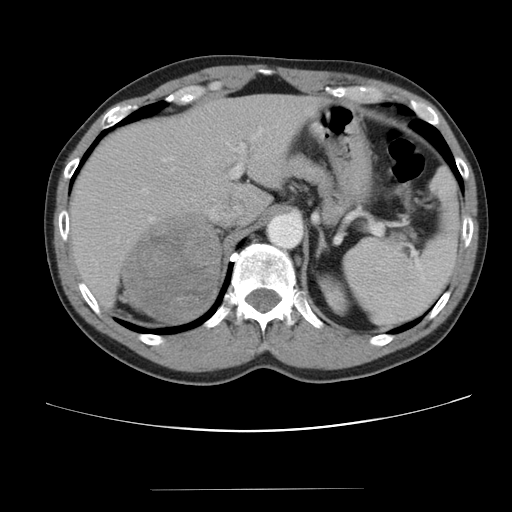
Contrast-enhanced abdominal CT, one axial slice. Position 68 of 80 along the scan axis. Reconstruction kernel STANDARD. 120 kVp. Intravenous contrast given. Soft-tissue window (W 400 / L 40 HU). 512 × 512 image matrix, field of view 360 × 360 mm. Patient: male, 61 years. From the clinical record (not read from this slice): diagnosis: adrenocortical carcinoma; tumour side: right adrenal; tumour size at pathology: 11.1 cm; Ki-67 index: 32 %; stage (as recorded): 2.
Structures marked on this image (semi-automatically segmented with operator editing):
- mass: bounding box [x1, y1, x2, y2] px = [123, 216, 219, 322]